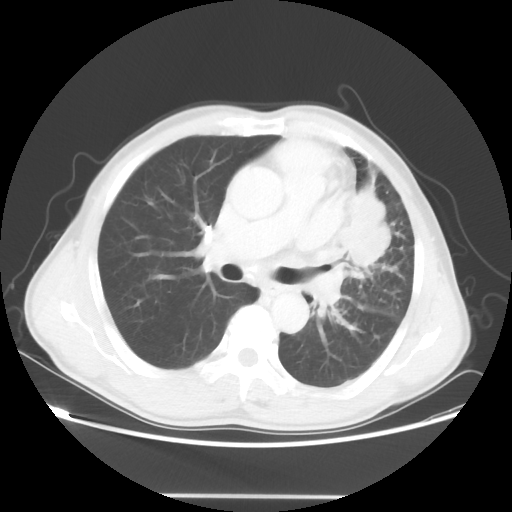
Chest CT, one axial slice. Position 30 of 55 along the scan axis. 100 kVp. Lung window (W 1500 / L -600 HU). 512 × 512 image matrix, field of view 398 × 398 mm. Patient: male, 60 years. From the clinical record (not read from this slice): clinical TNM (as recorded): T3 N3 M0.
Outlined on this slice (bounding box drawn by a radiologist):
- lung tumour (recorded histology: adenocarcinoma): box from (x=341, y=178) to (x=387, y=270) px